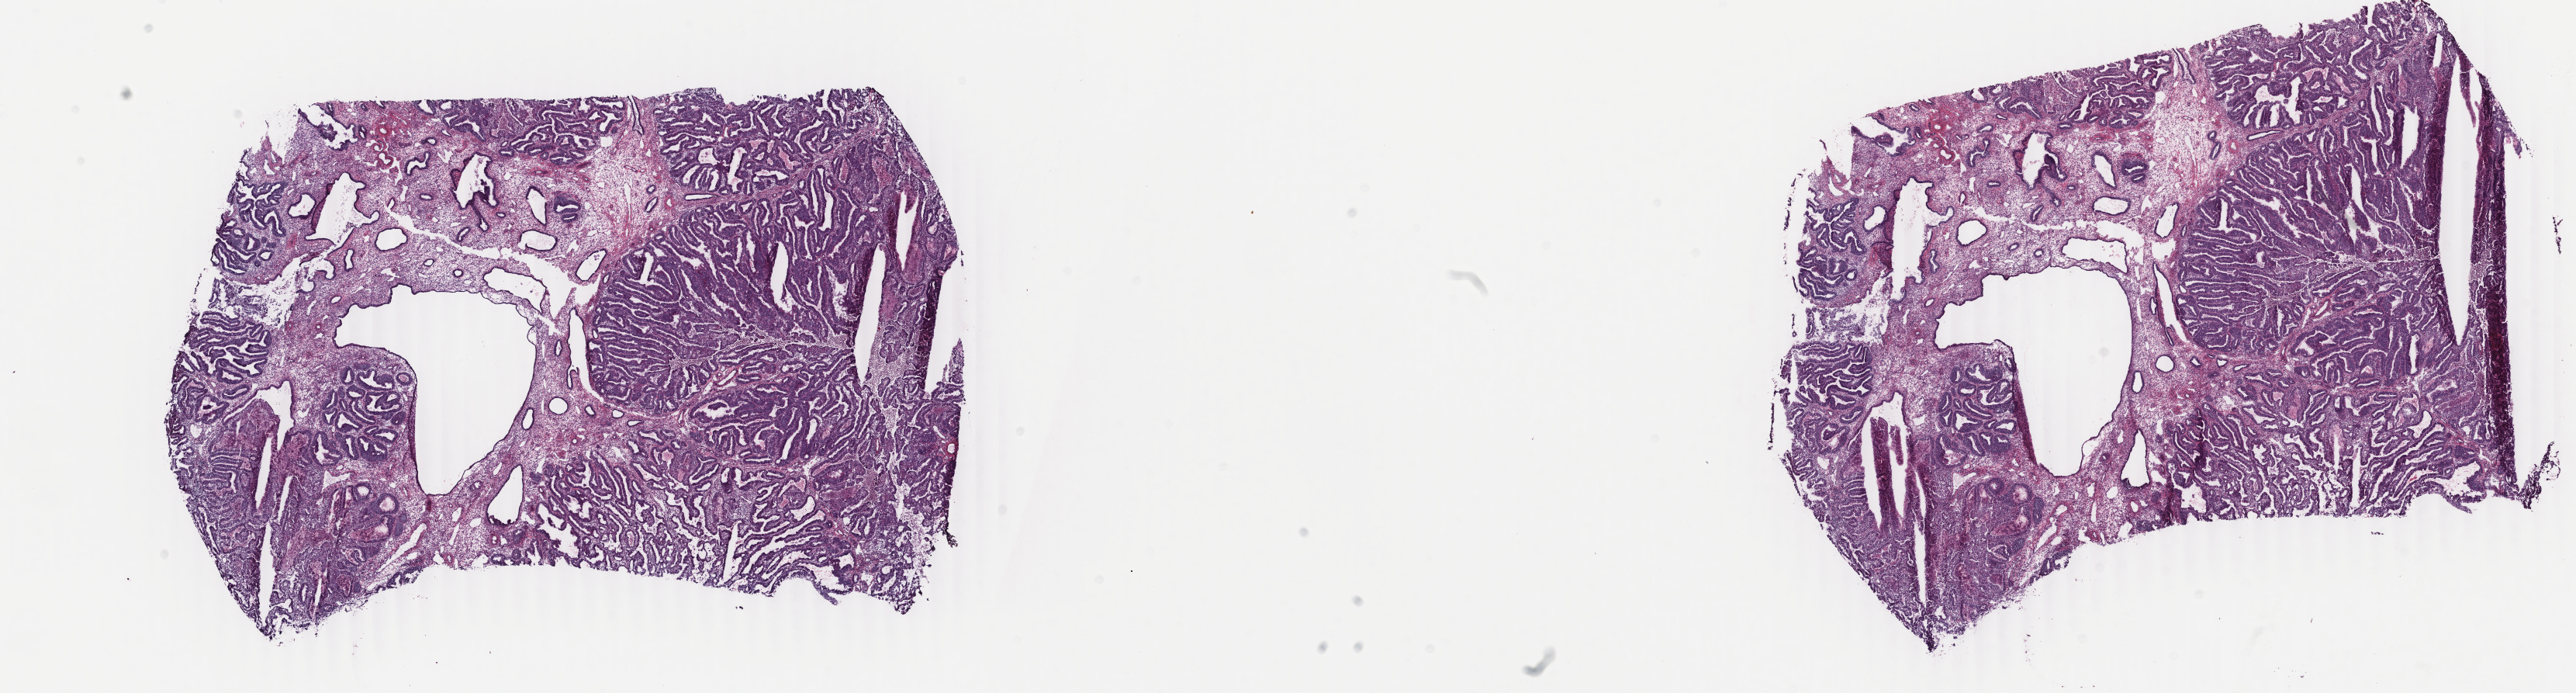
H&E-stained whole-slide image, low-resolution overview of the scanned area, about 26.4 x 7.1 mm (acquisition: 40x scan); frozen section; uterus, primary tumour sample. Female, age 57 years at initial diagnosis. Histologic grade: G2 (moderately differentiated). Slide review estimates, as recorded: tumour cells 60%, tumour nuclei 70%, normal cells 0%, stromal cells 30%, necrosis 10%. Infiltration values recorded for this section: lymphocyte infiltration 20%, monocyte infiltration 0%, neutrophil infiltration 20%.
FIGO stage: IB. Histologic diagnosis: Endometrioid adenocarcinoma, NOS (endometrium). Lymph nodes positive (case pathology): 0 of 48 examined.